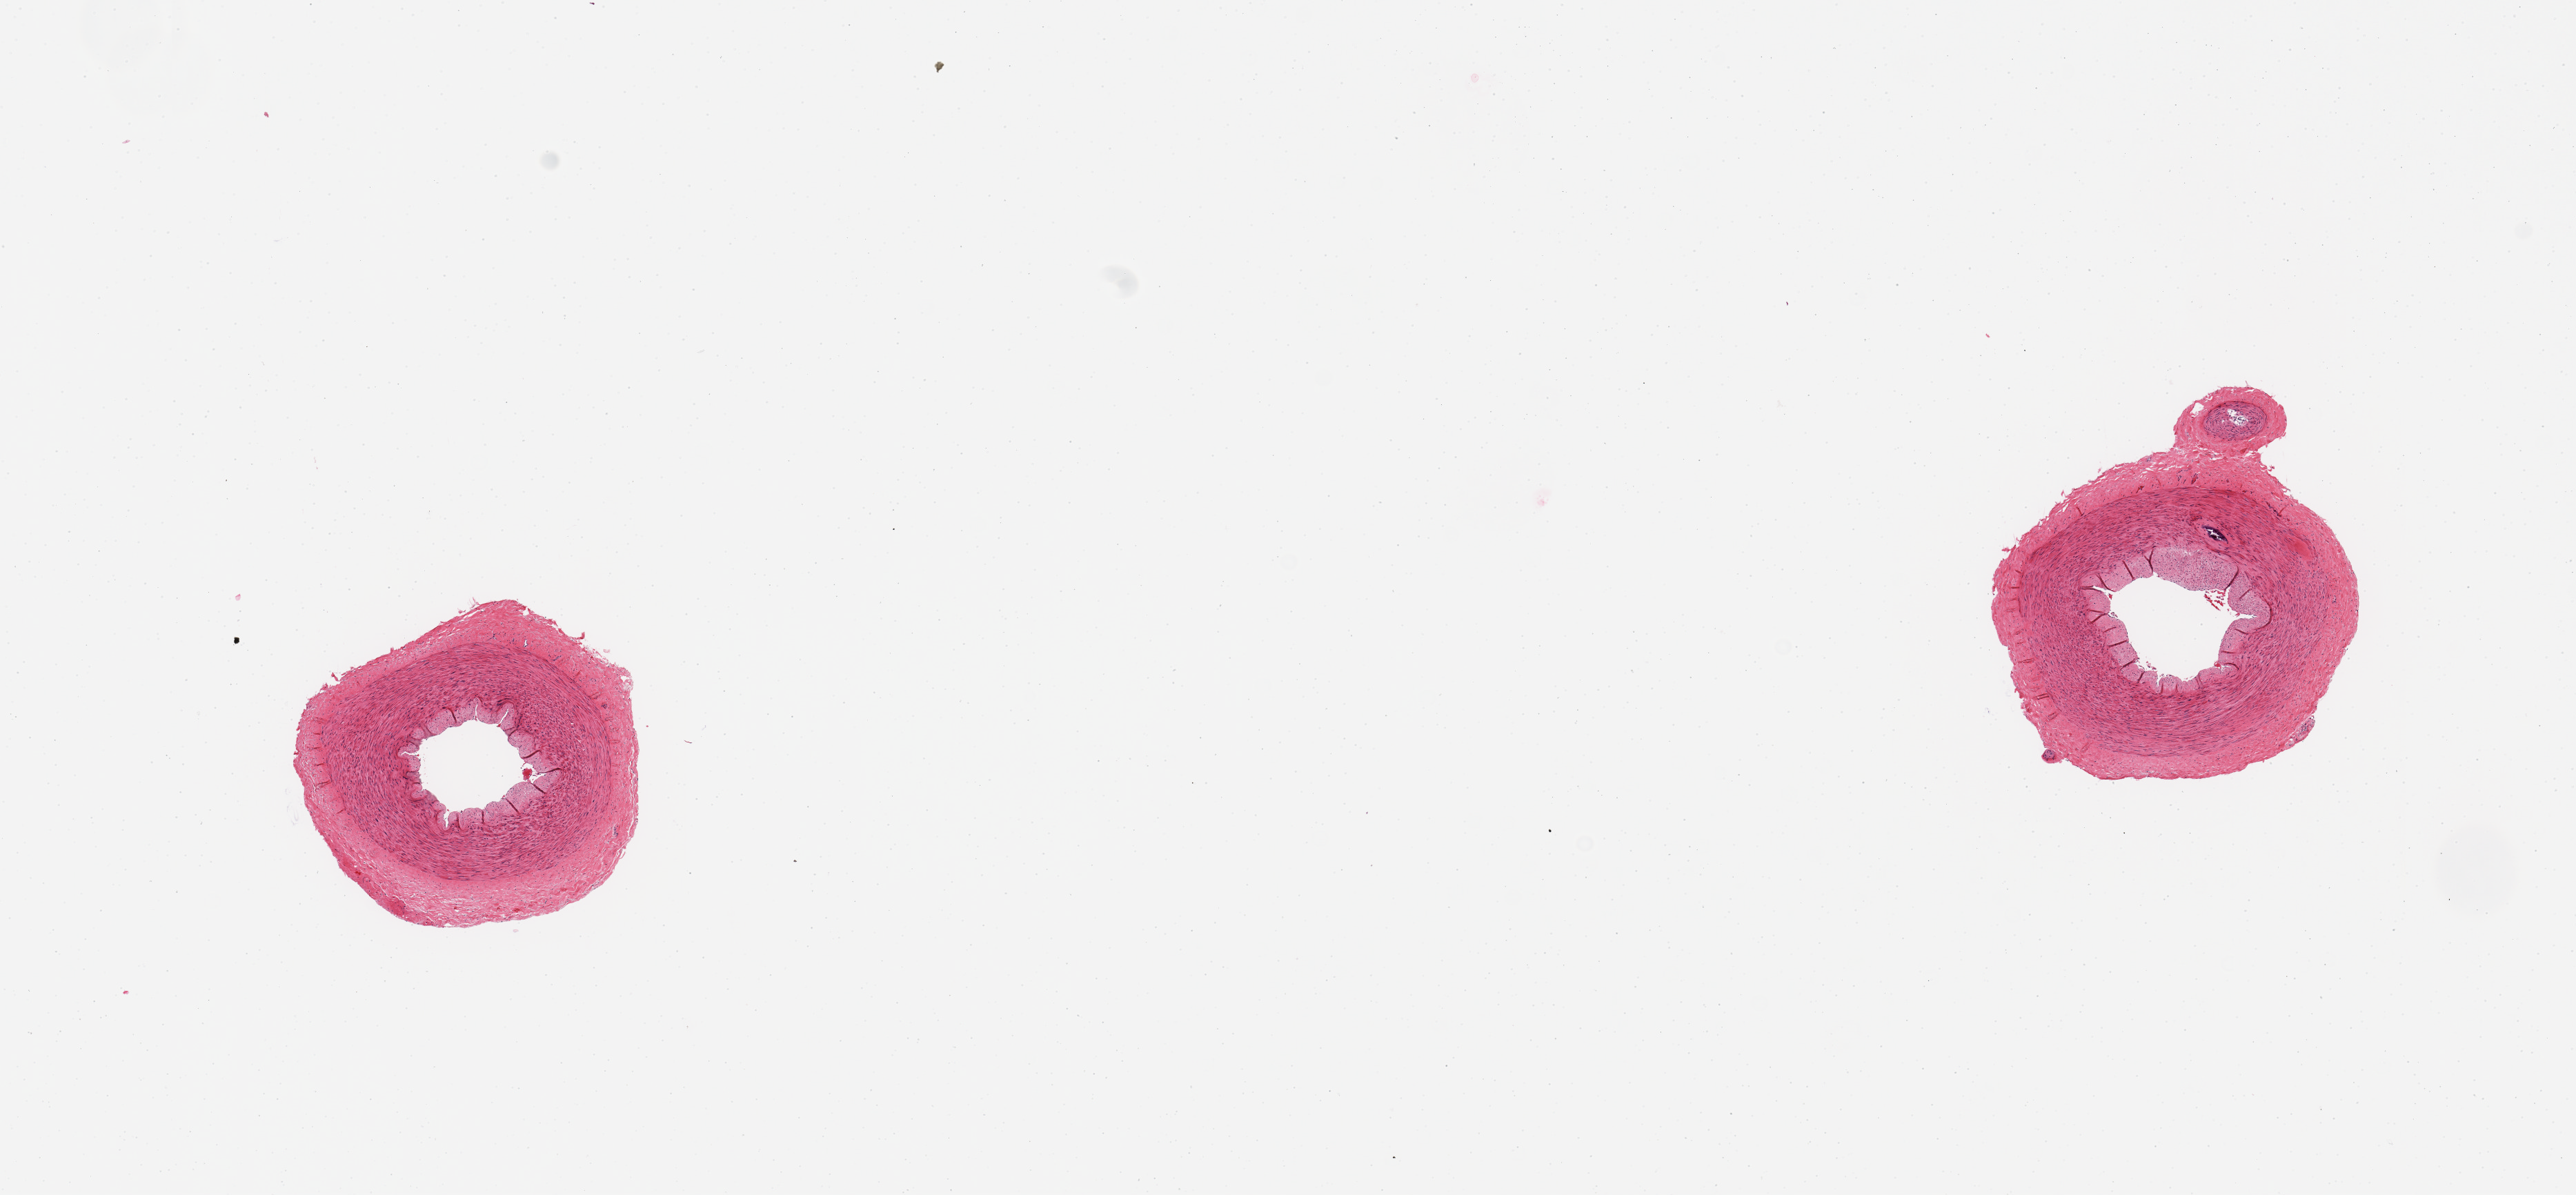
Hematoxylin and eosin (H&E) whole-slide image, brightfield — a low-resolution overview of the entire scanned area, about 14.8 x 6.8 mm (from a 20x scan). PAXgene-fixed, paraffin-embedded tissue. Sampled site (target tissue): tibial artery. Tissue donor sample.
Pathologist's review note for this sample: 2 pieces; no plaque; small (0.15 mm) focal medial calcium deposit; well trimmed.